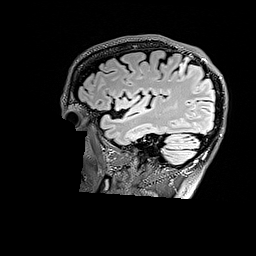
Brain MRI from a brain-tumour surgery series, one sagittal slice; slice 129 of 176 in the series (ordered by position); T2 FLAIR; 1 mm slice thickness; 256 × 256 image matrix, field of view 256 × 256 mm. Case-level facts recorded for this patient, not image findings: histopathology: Astrocytoma; WHO grade: 3; IDH mutation: yes; tumour location: Right Parietal.
Outlined on this slice (manually delineated by an expert):
- tumour: bounding box <179,62,186,74> (left, top, right, bottom; pixels)